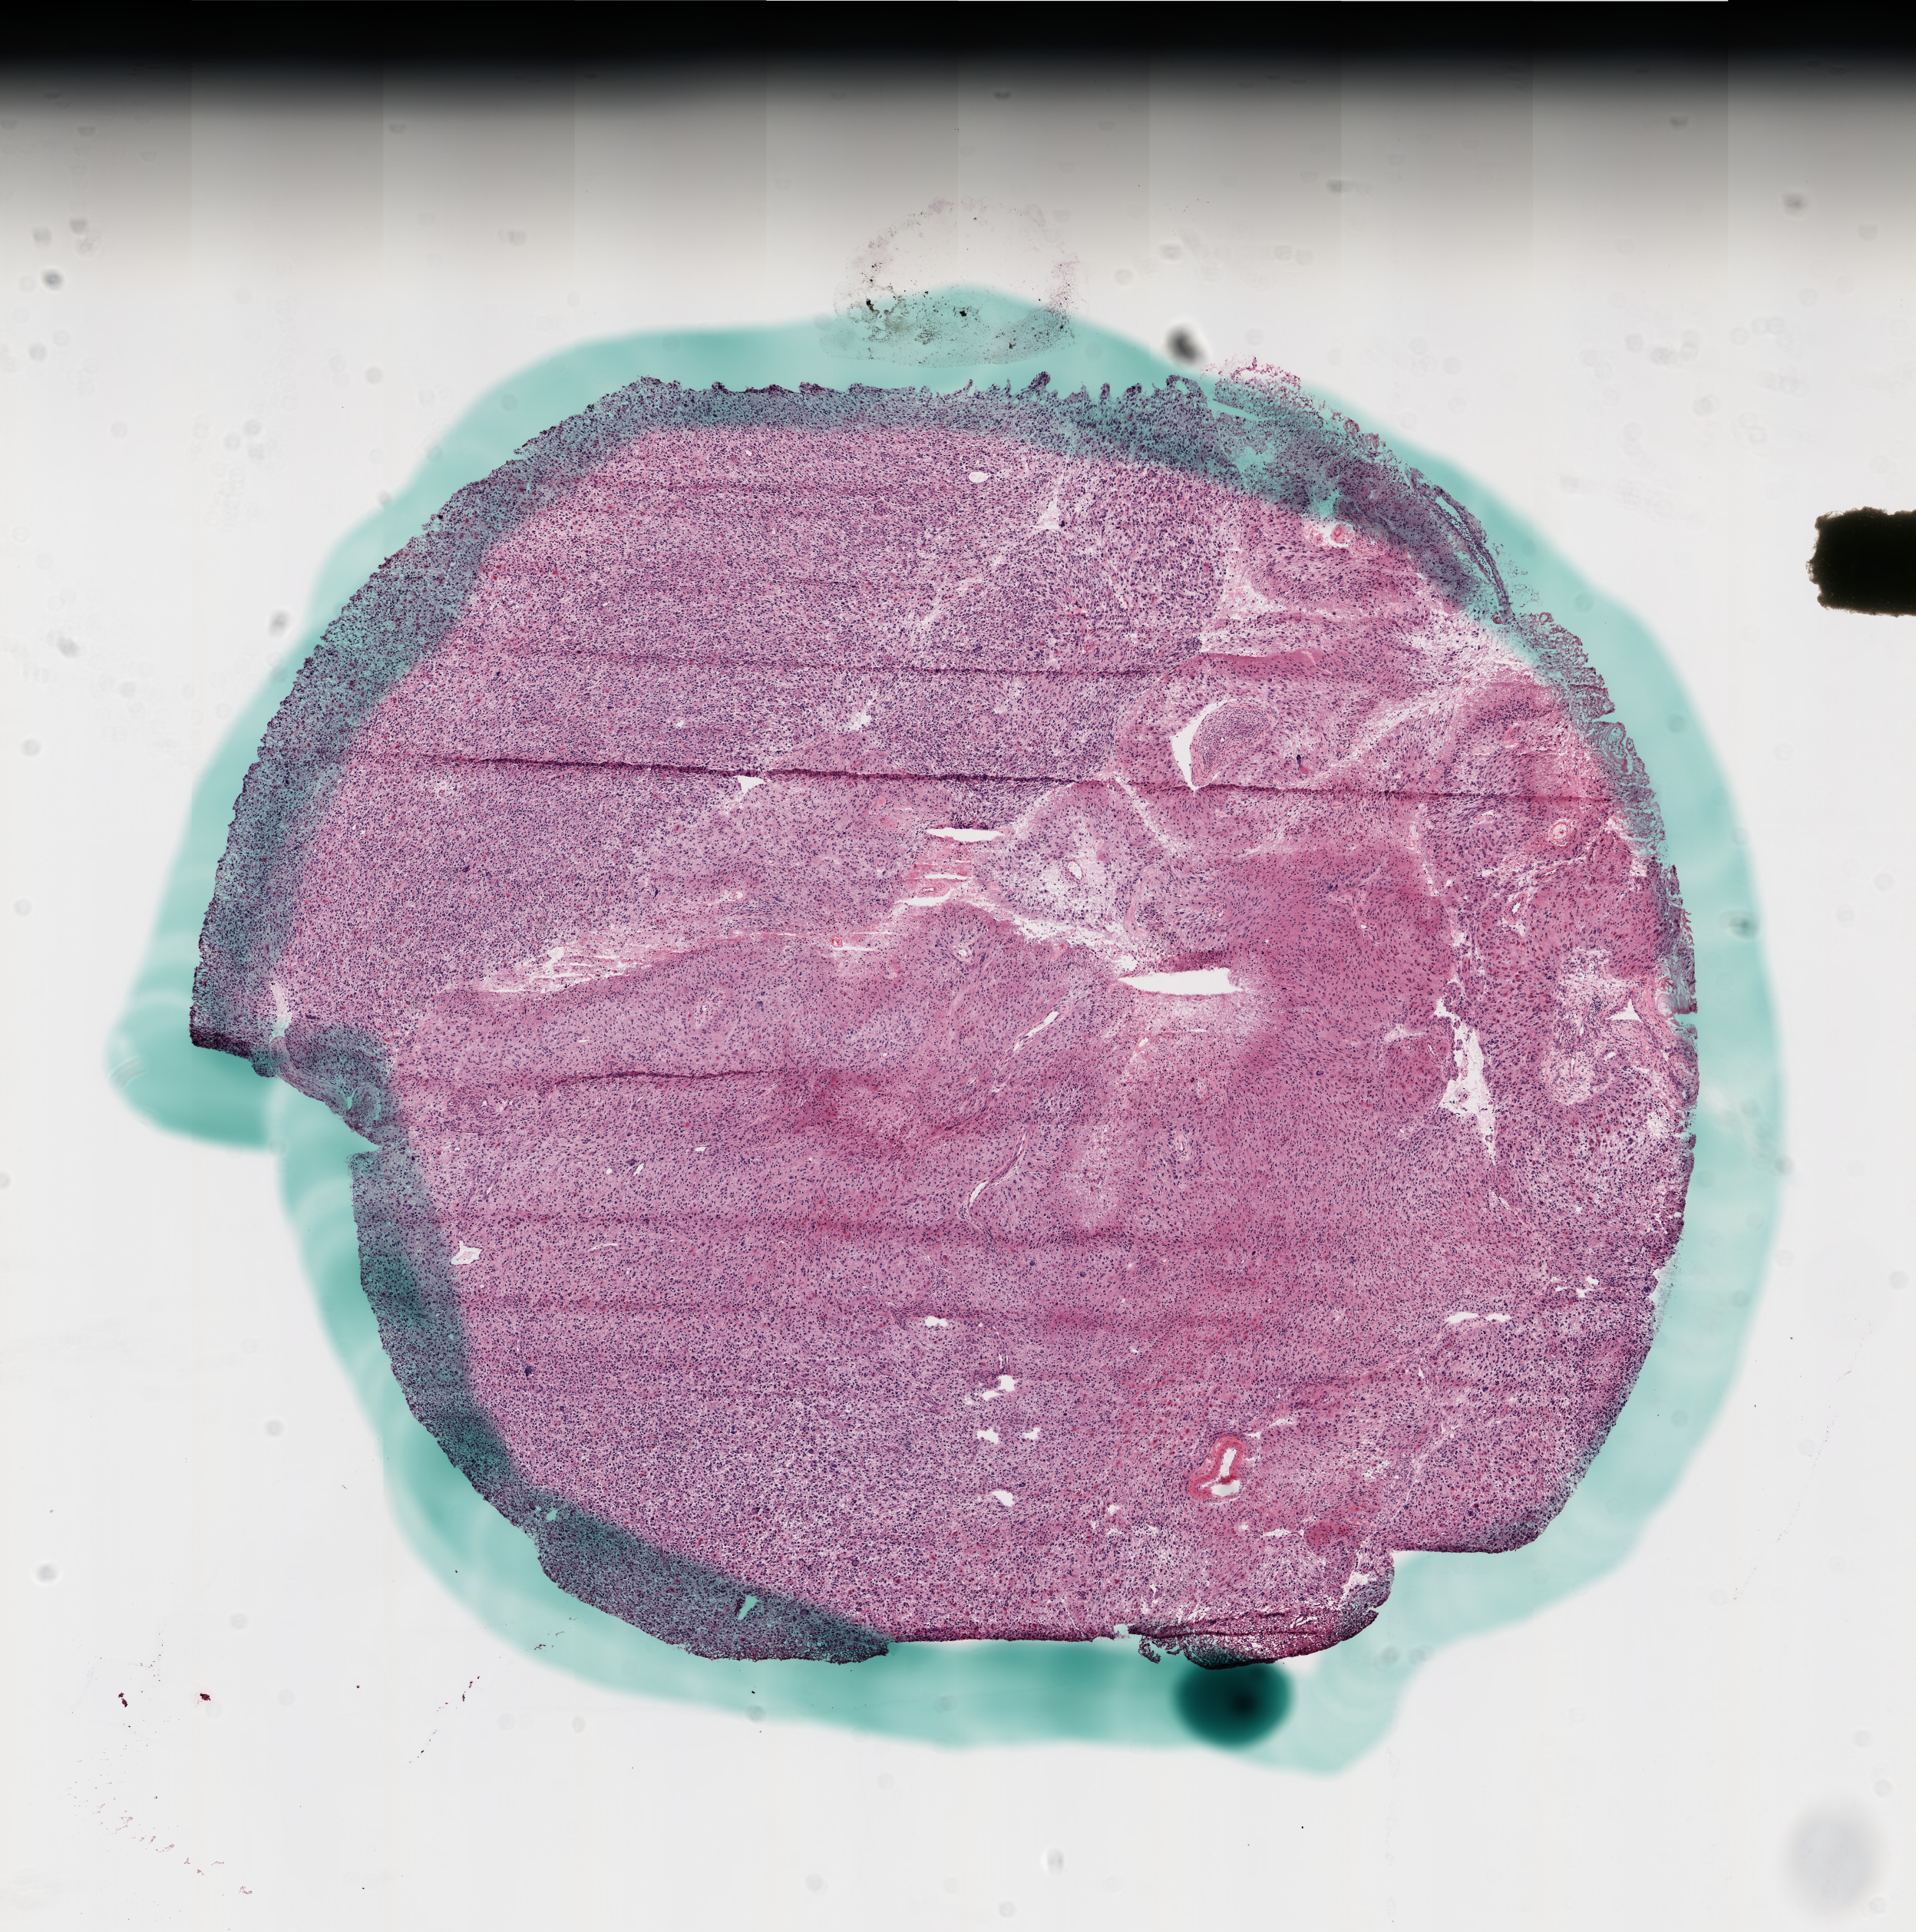
H&E whole-slide image, low-resolution overview of the scanned area, about 10.0 x 10.1 mm (from a 20x scan), frozen section, primary tumour sample from the brain. Male, age 69 years at initial diagnosis. Slide review estimates, as recorded: tumour cells 90%, tumour nuclei 100%, normal cells 0%, stromal cells 0%, necrosis 10%.
Histologic diagnosis: Glioblastoma.